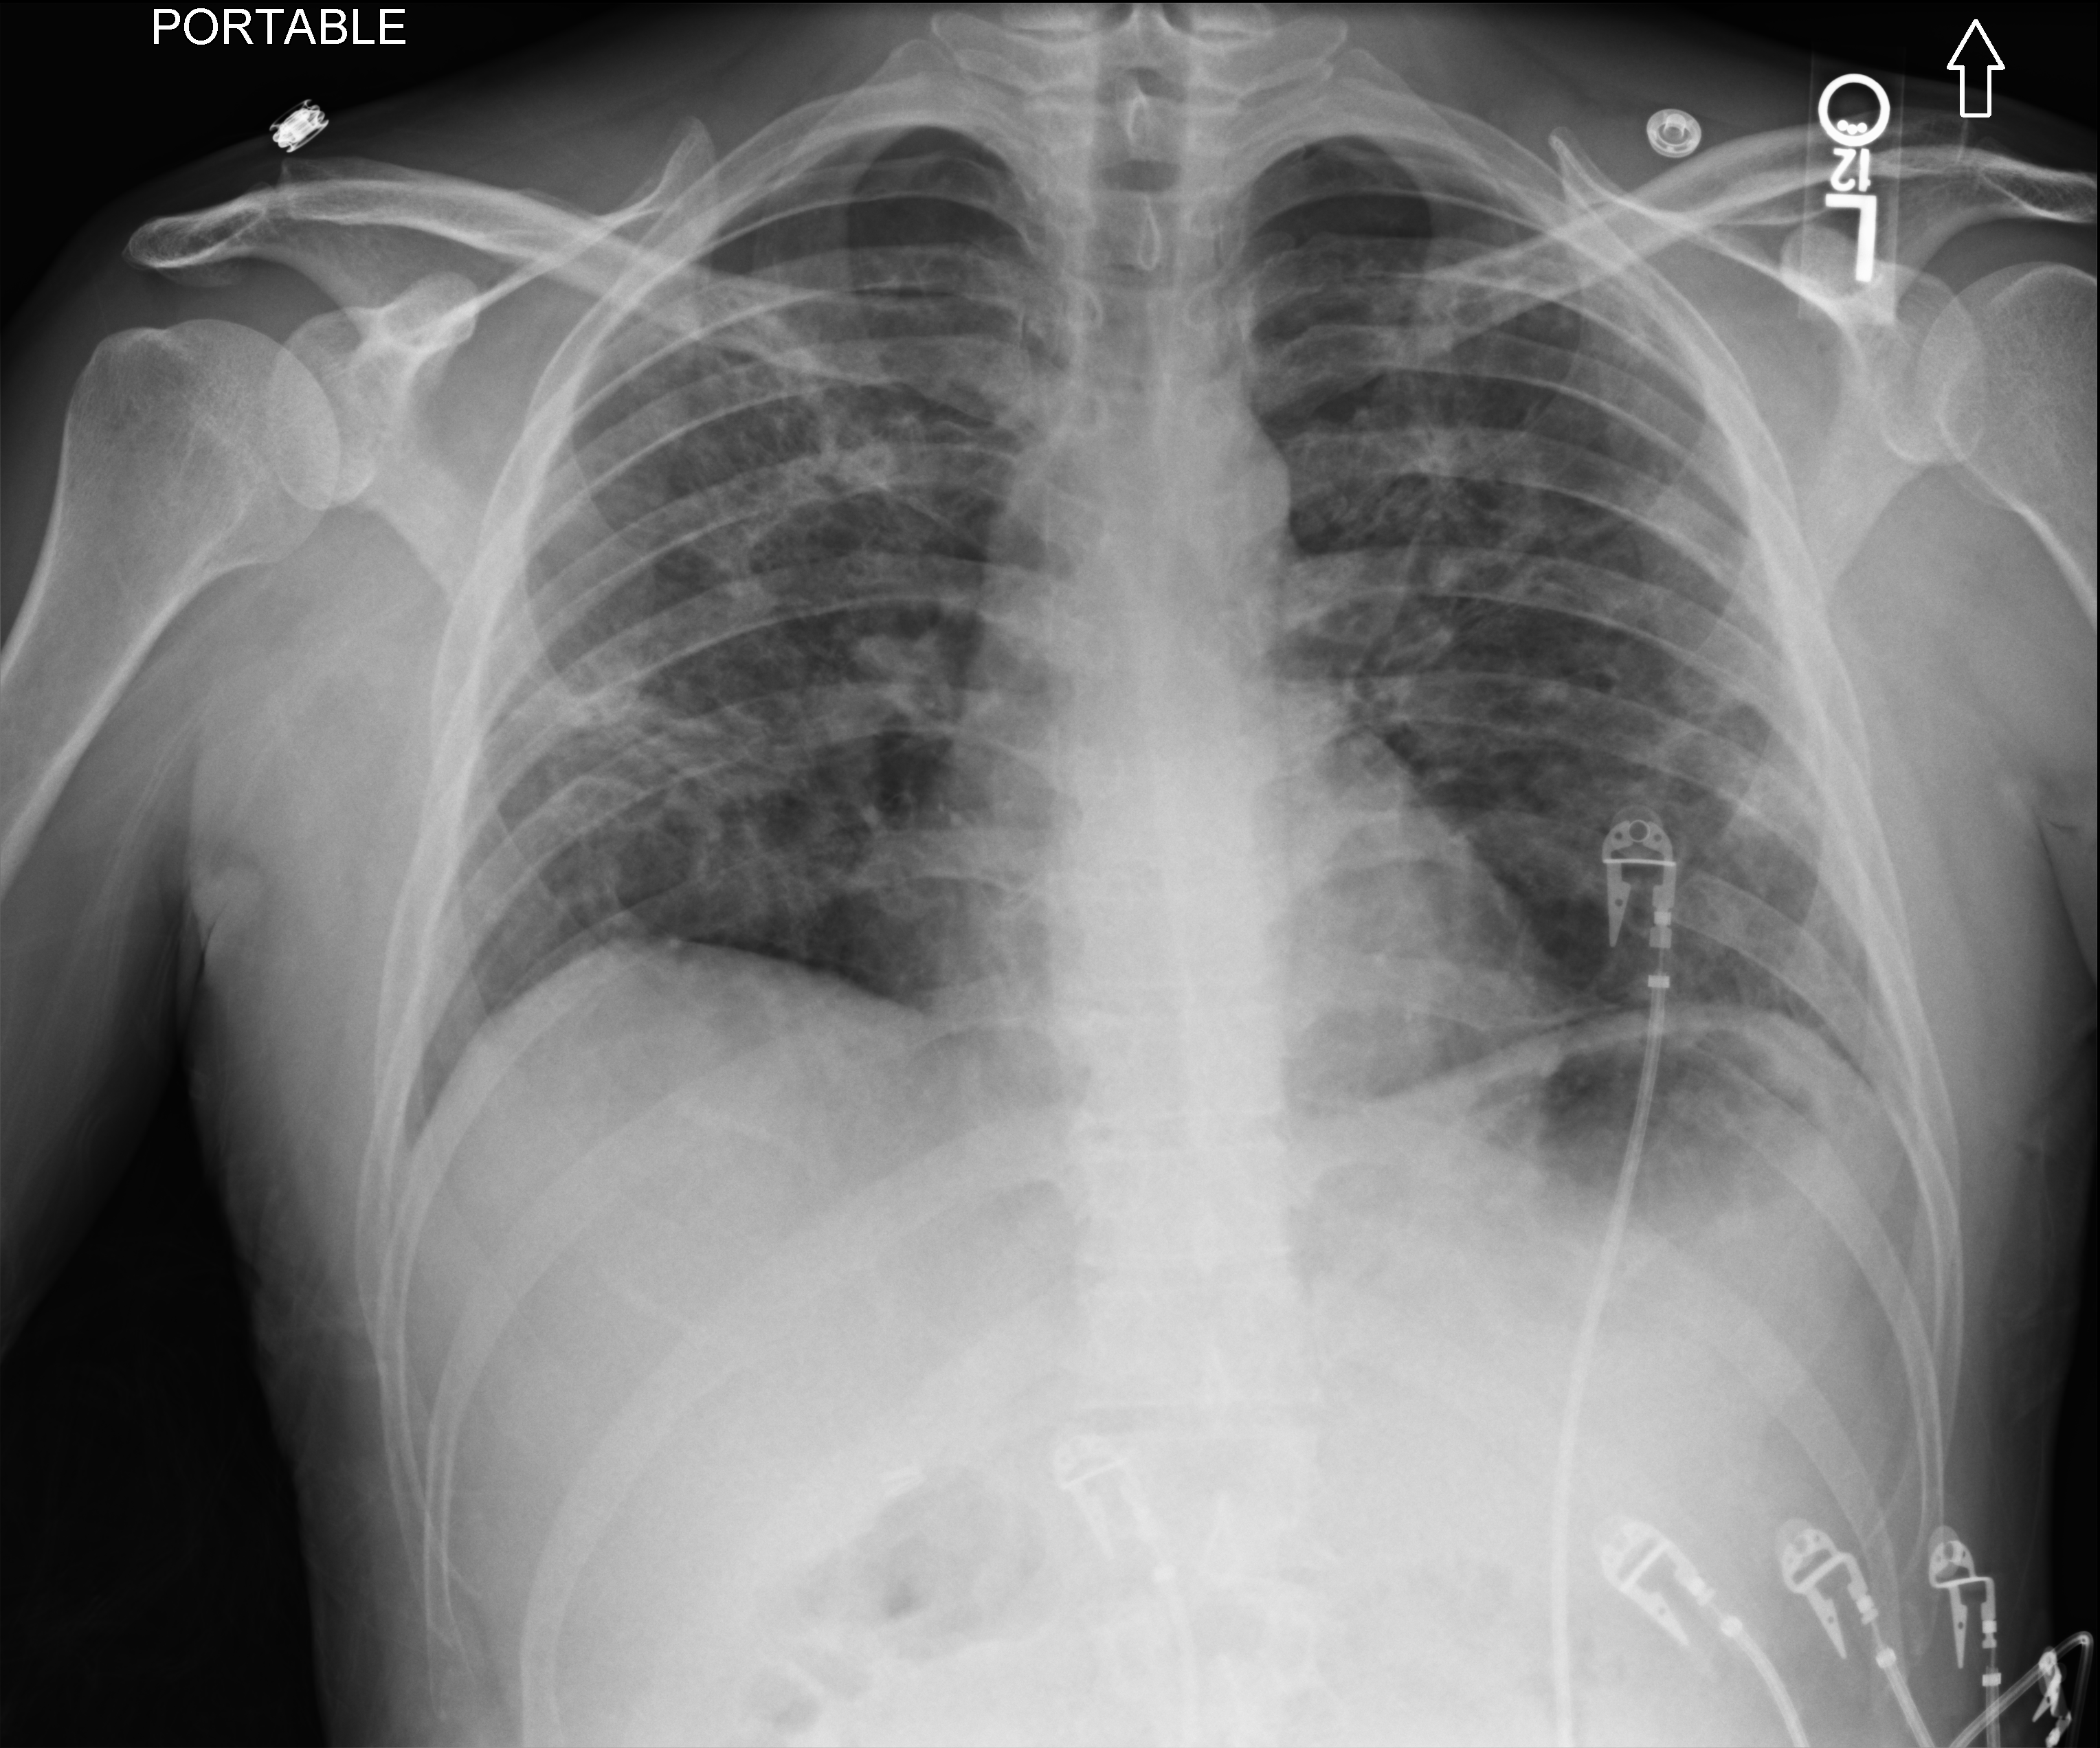
Chest X-ray (portable), anteroposterior (AP) projection. Male patient hospitalised with COVID-19, age 18–59 years.
Hospital-stay facts (about this admission, not read from this image; timing relative to this image not recorded): diabetes (admission record): no; admitted to intensive care during this hospital stay: yes.